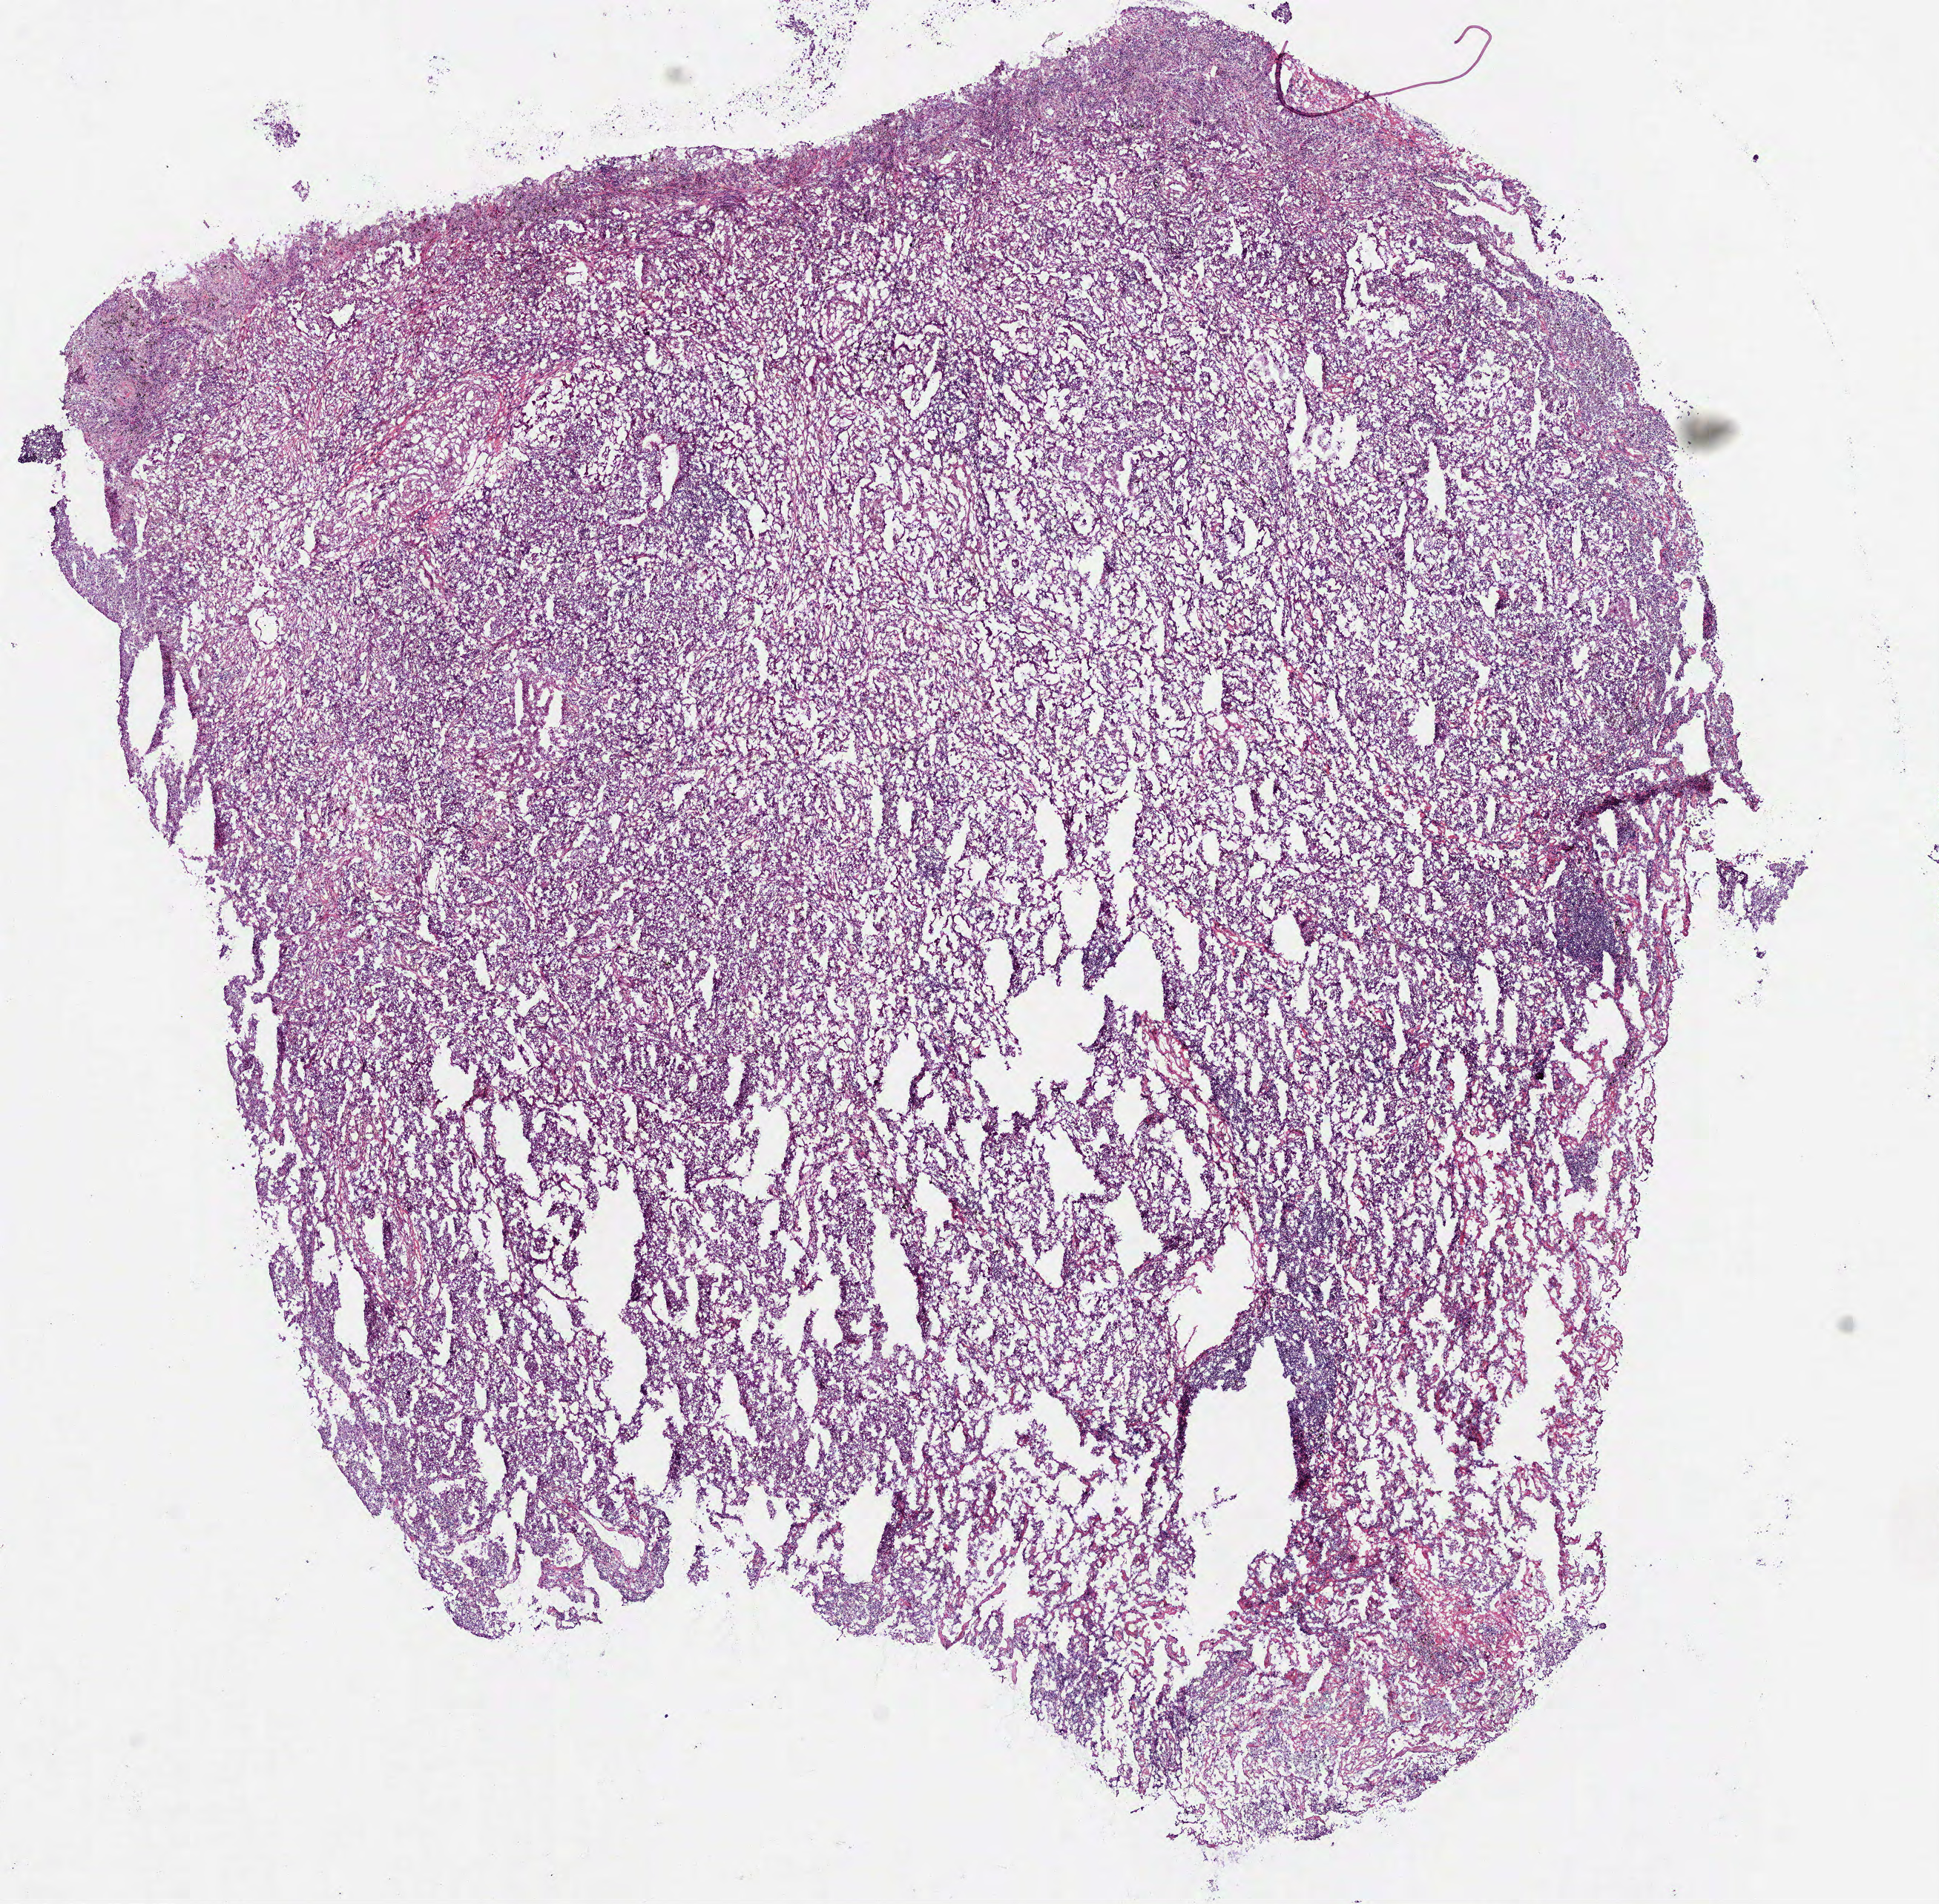
Whole-slide histology image, H&E-stained — shown as a low-resolution overview of the whole scanned area (about 10.5 x 10.4 mm). Frozen section. Lung, primary tumour sample. Female, age 55 years at initial diagnosis. Slide review estimates, as recorded: tumour cells 84%, tumour nuclei 71%, normal cells 4%, stromal cells 8%, necrosis 4%. Inflammatory infiltration, as recorded: lymphocyte infiltration 10%, monocyte infiltration 5%, neutrophil infiltration 5%.
AJCC pathologic stage: IIIA (7th edition). Laterality: right. Pathologic diagnosis: Adenocarcinoma, NOS (upper lobe, lung).